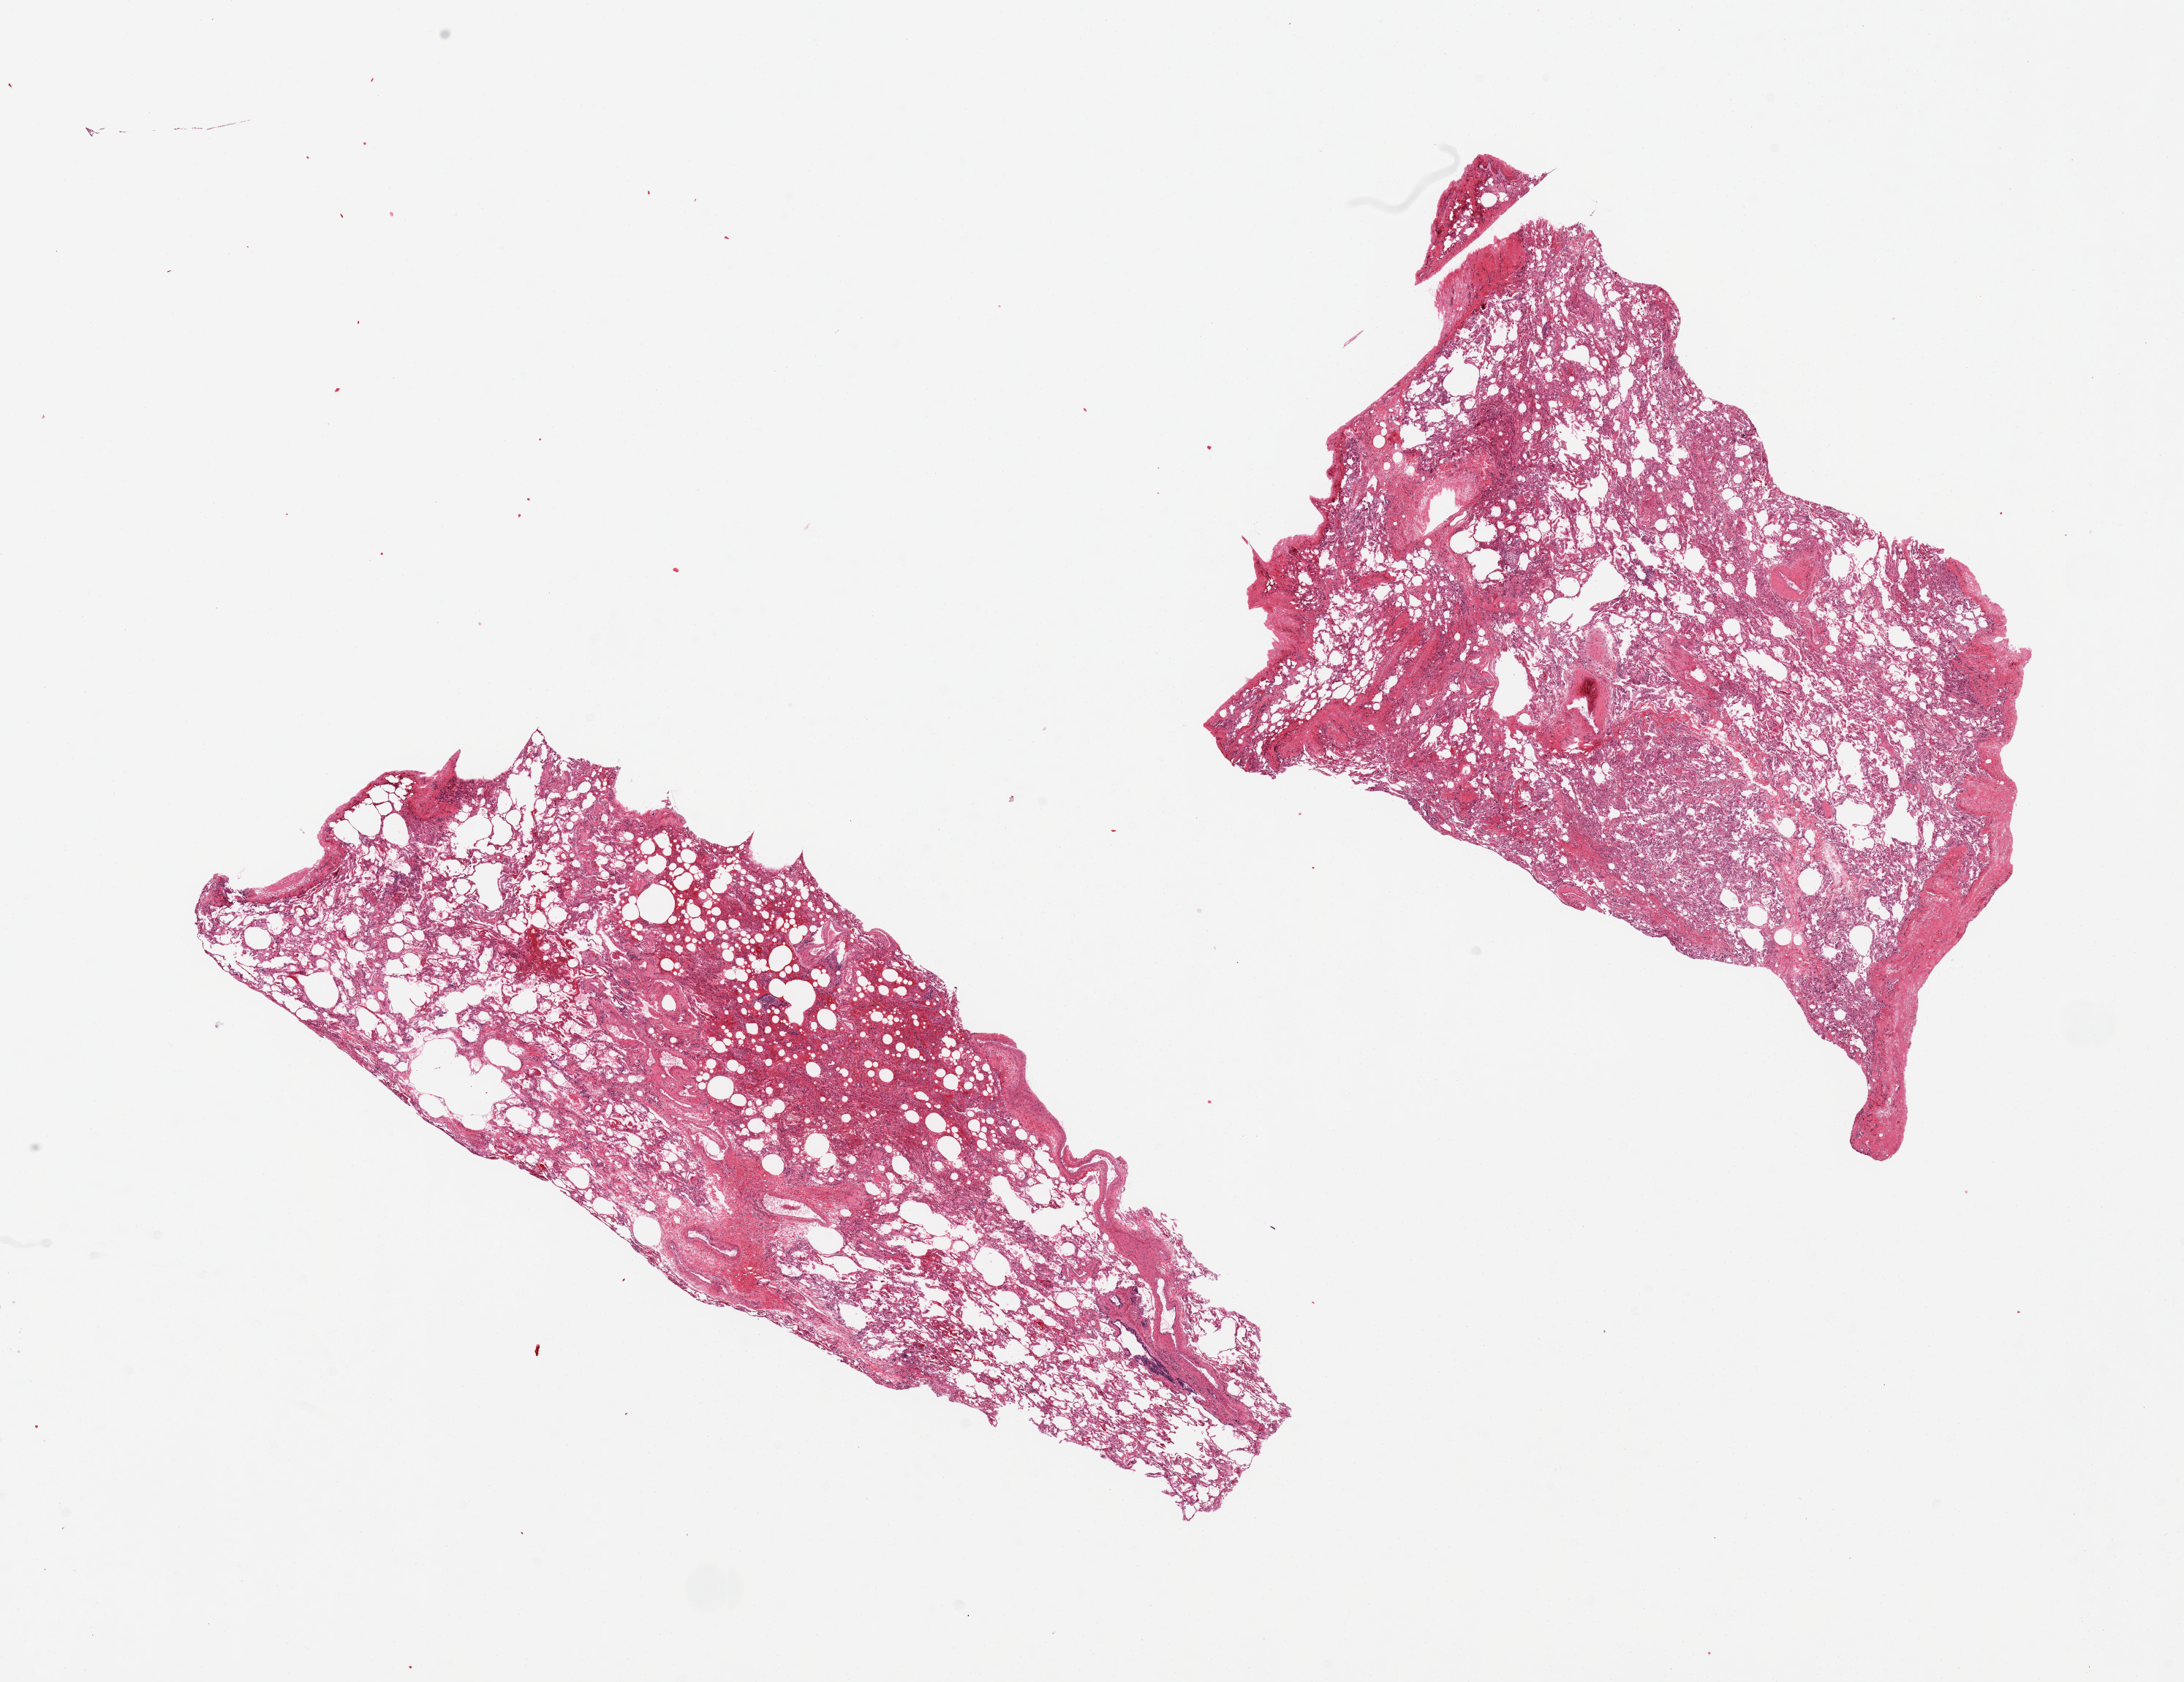
Digitized H&E-stained section, brightfield, low-resolution overview of the scanned area, about 23.6 x 18.2 mm (slide scanned at 20x). PAXgene-fixed paraffin-embedded (PFPE) section. Section of lung (target tissue). Donor tissue sample. Donor: female.
Review note (as recorded): 2 pieces, mild congestion.